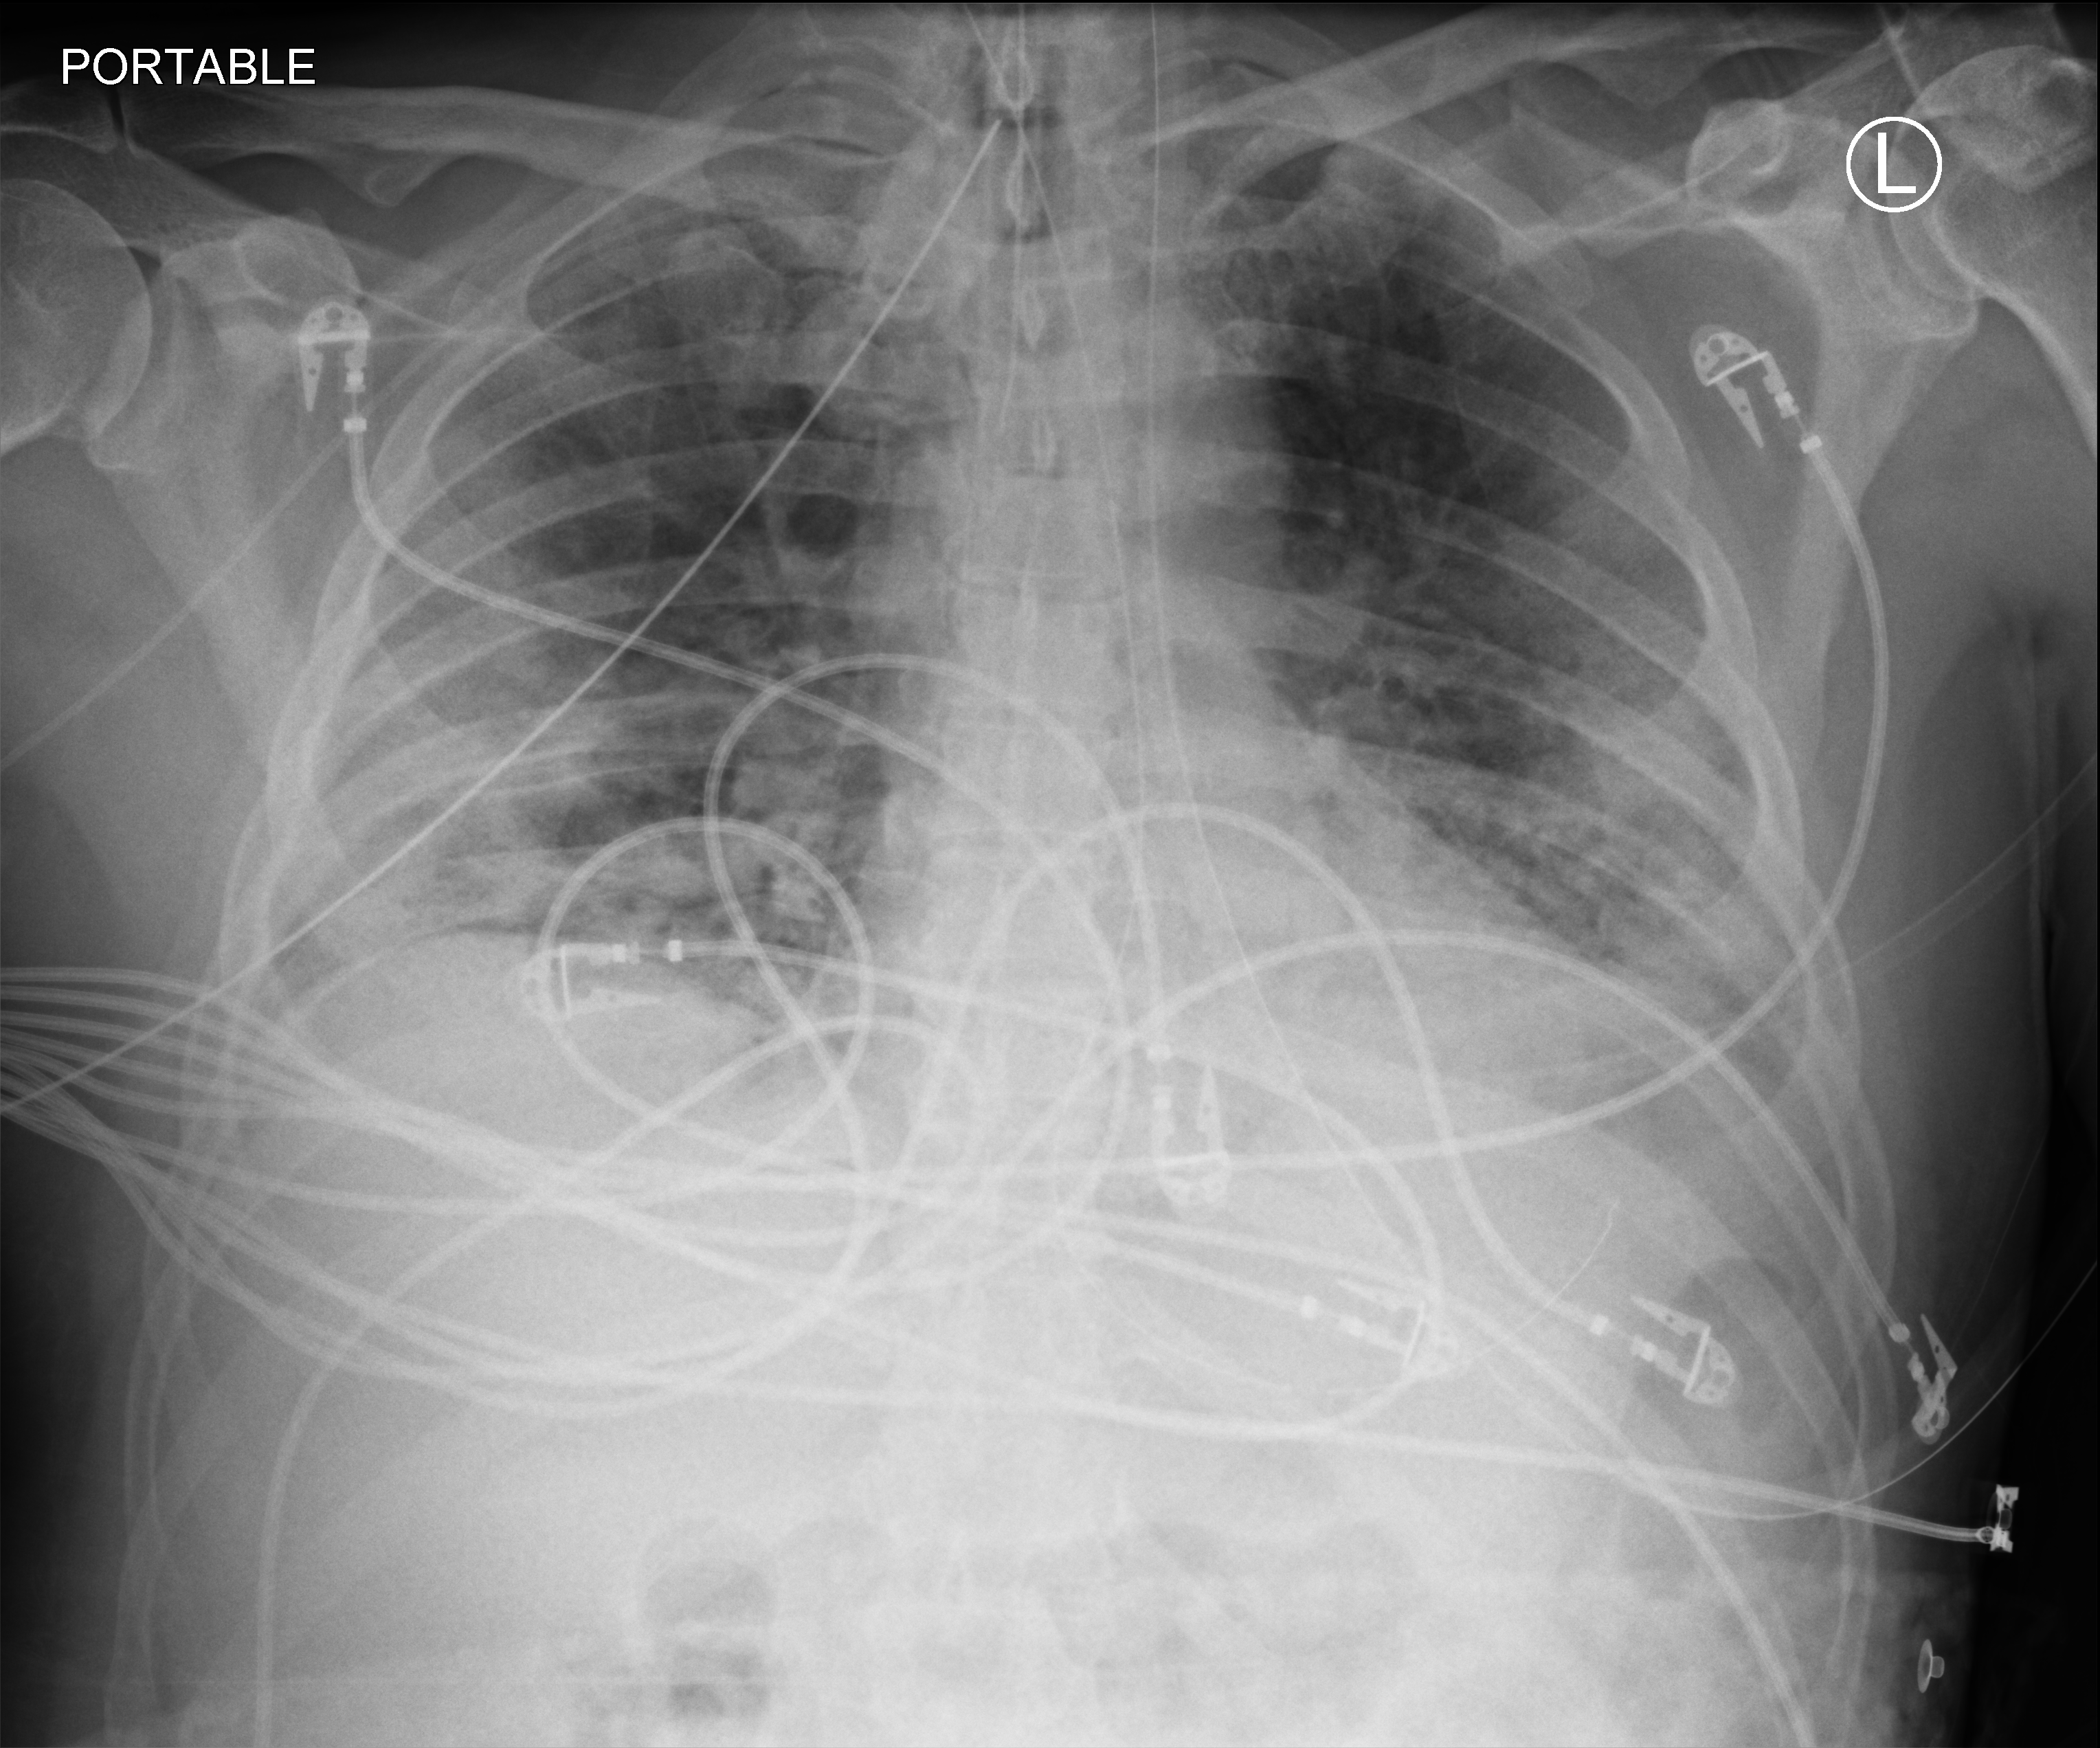
Chest X-ray (portable), anteroposterior (AP) projection. Patient hospitalised with COVID-19; male, aged 60–74 years.
Hospital-stay facts (about this admission, not read from this image; timing relative to this image not recorded):
- hypertension (admission record): no
- mechanically ventilated during this hospital stay: yes
- chronic kidney disease (admission record): no